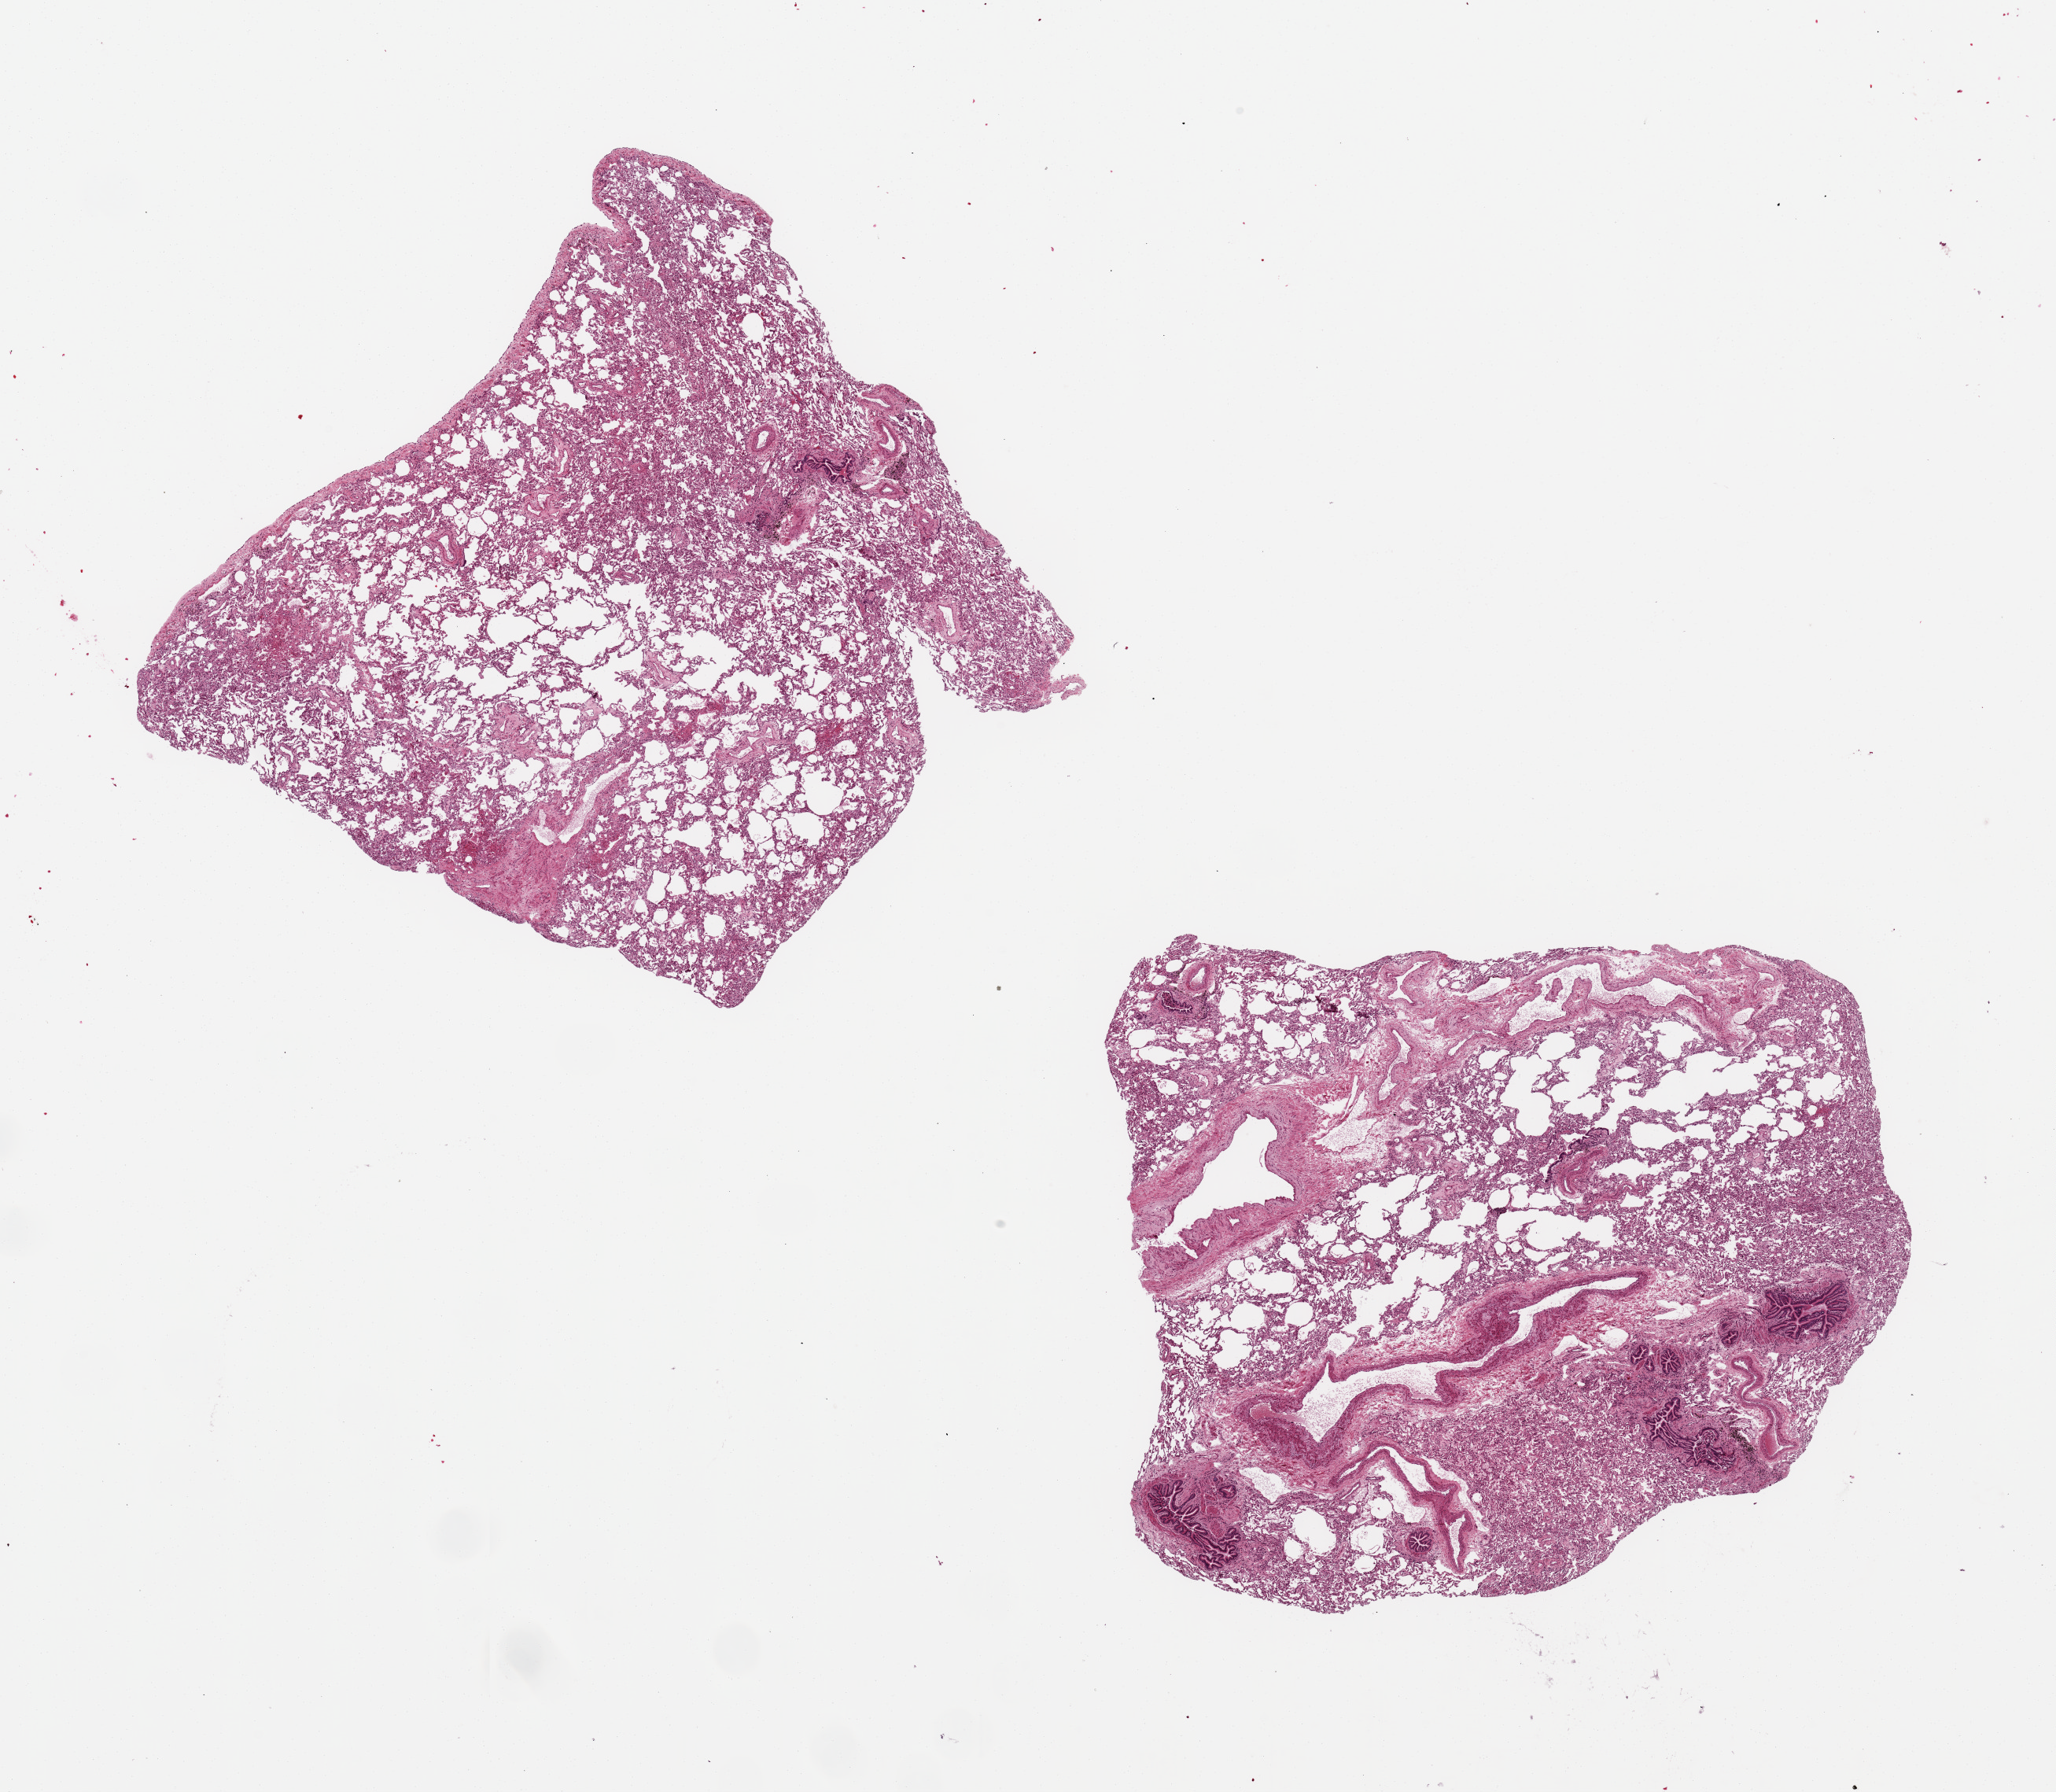
Hematoxylin and eosin (H&E) whole-slide image, brightfield, whole scanned area (about 20.7 x 18.0 mm) shown as a low-resolution overview, PAXgene-fixed, paraffin-embedded tissue, section of lung (target tissue), tissue donor sample. Male donor.
* review note (as recorded): 2 pieces, 8x7mm